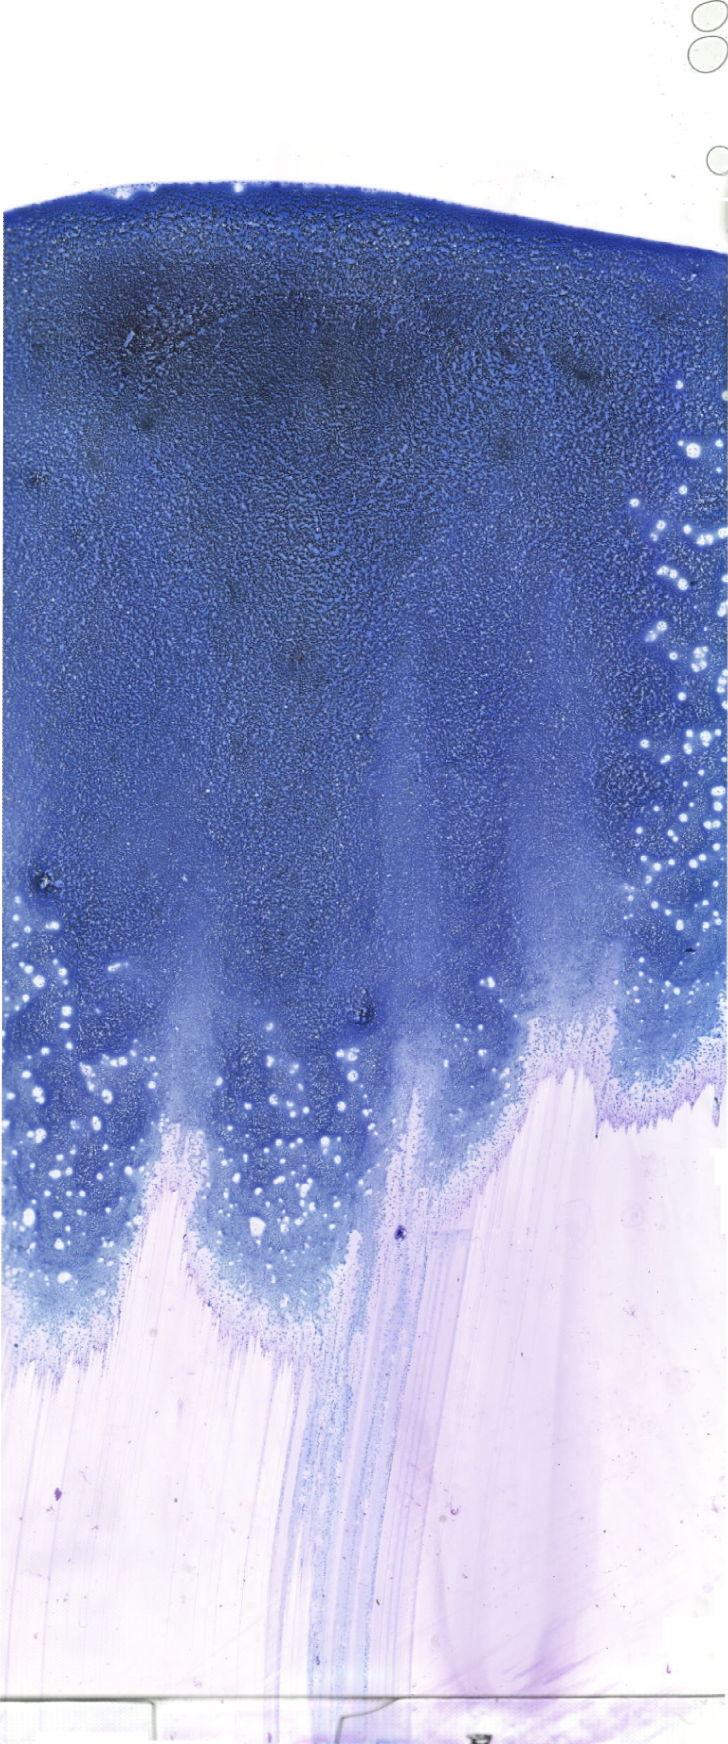
Bone marrow aspirate smear, May-Grünwald–Giemsa stain, whole-slide image — shown as a low-resolution overview of the whole scanned area (about 20.6 x 49.4 mm). Female patient.
Diagnosis: Acute Myeloid Leukemia with Maturation.